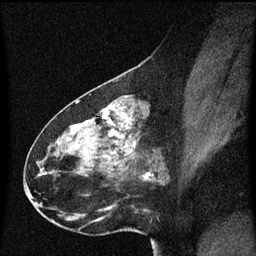
Breast MRI (dynamic contrast-enhanced), one sagittal slice. Position 28 of 60 along the scan axis. Dynamic contrast-enhanced series, image 2 of 3 at this slice position (ordered by acquisition). 1.5 T. TE 4.2 ms, TR 8.4 ms. 256 × 256 image matrix, field of view 200 × 200 mm. Patient: female, 49 years. From the clinical record (not read from this slice): setting: breast cancer imaged before/during neoadjuvant chemotherapy; receptor status: HR-positive, HER2-negative.
Outlined on this slice (semi-automatic segmentation, software-assisted and operator-edited):
- analysis volume of interest (the breast-tissue region the enhancement analysis was run in; not a lesion): box from (x=27, y=96) to (x=170, y=221) px
- tumour enhancement mask (voxels above the 70 % enhancement threshold inside the analysis volume of interest): (x=104, y=110)–(x=136, y=161)